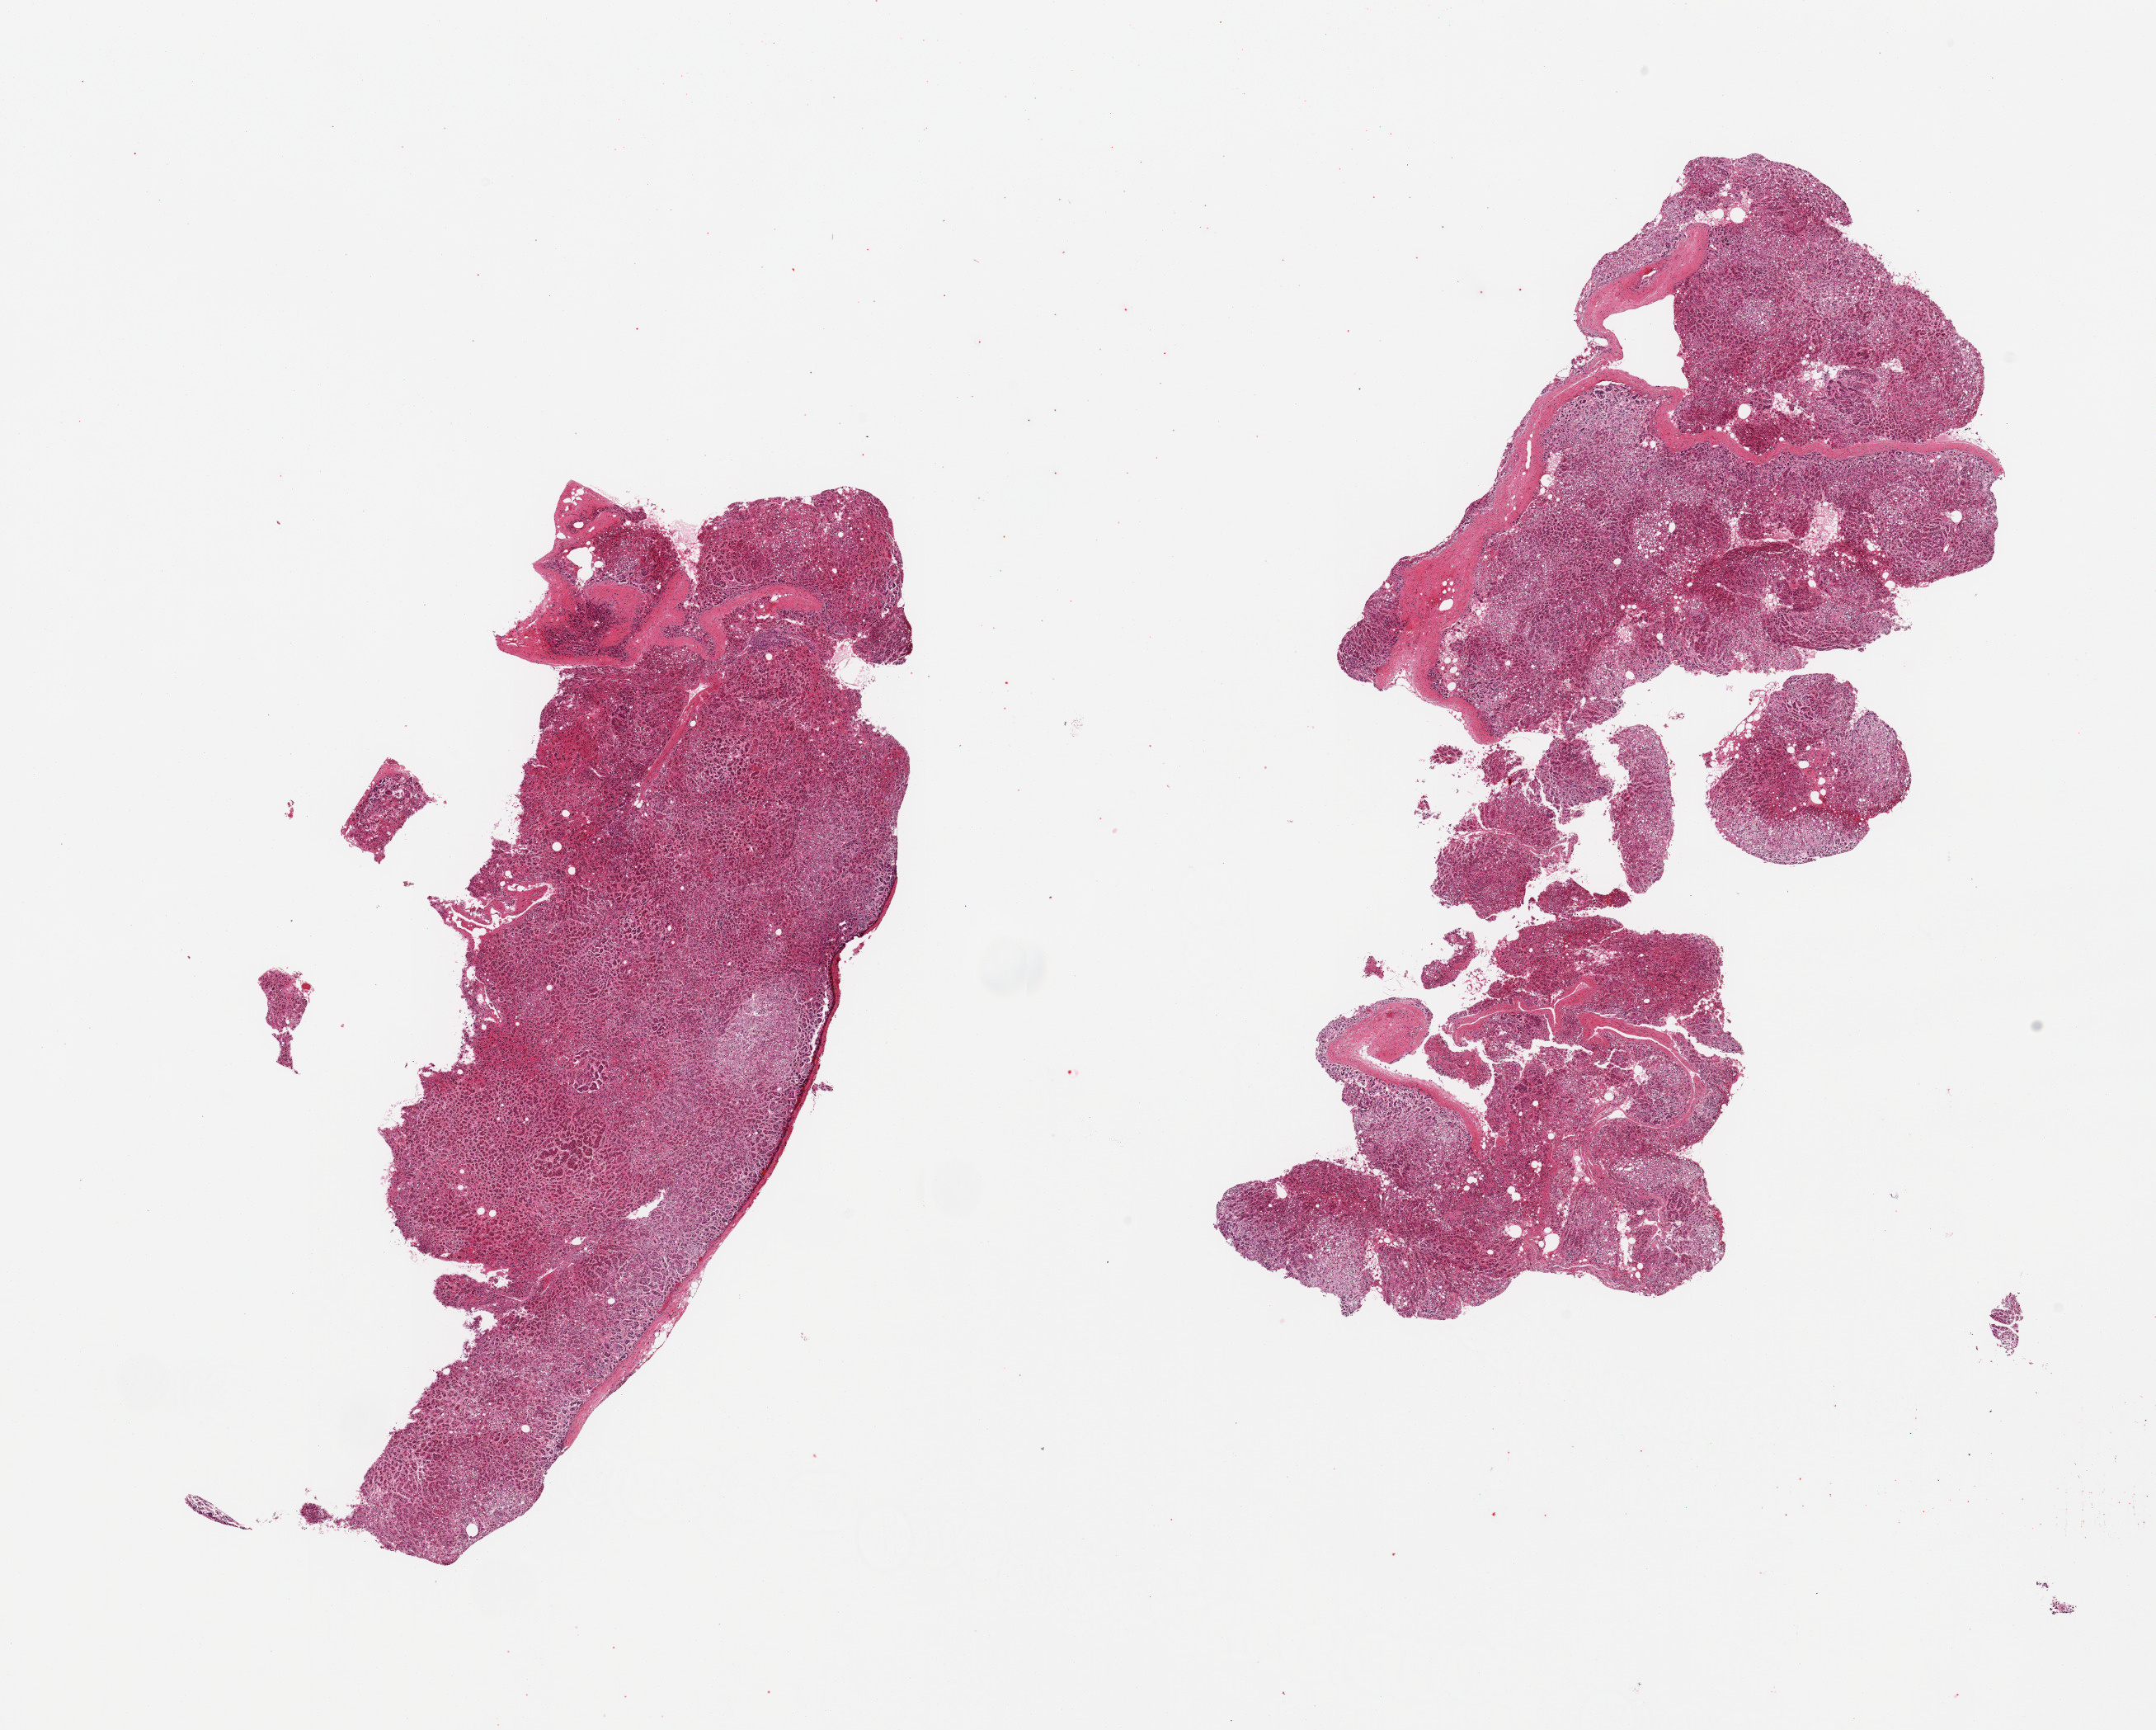
Digitized H&E-stained section, brightfield, shown as a low-resolution overview of the whole scanned area (about 20.7 x 16.6 mm), PAXgene-fixed paraffin-embedded (PFPE) section, sampled site (target tissue): adrenal gland, donor tissue sample. Donor: male.
Reviewer comment on this tissue sample: 2 pieces, one fragmented.